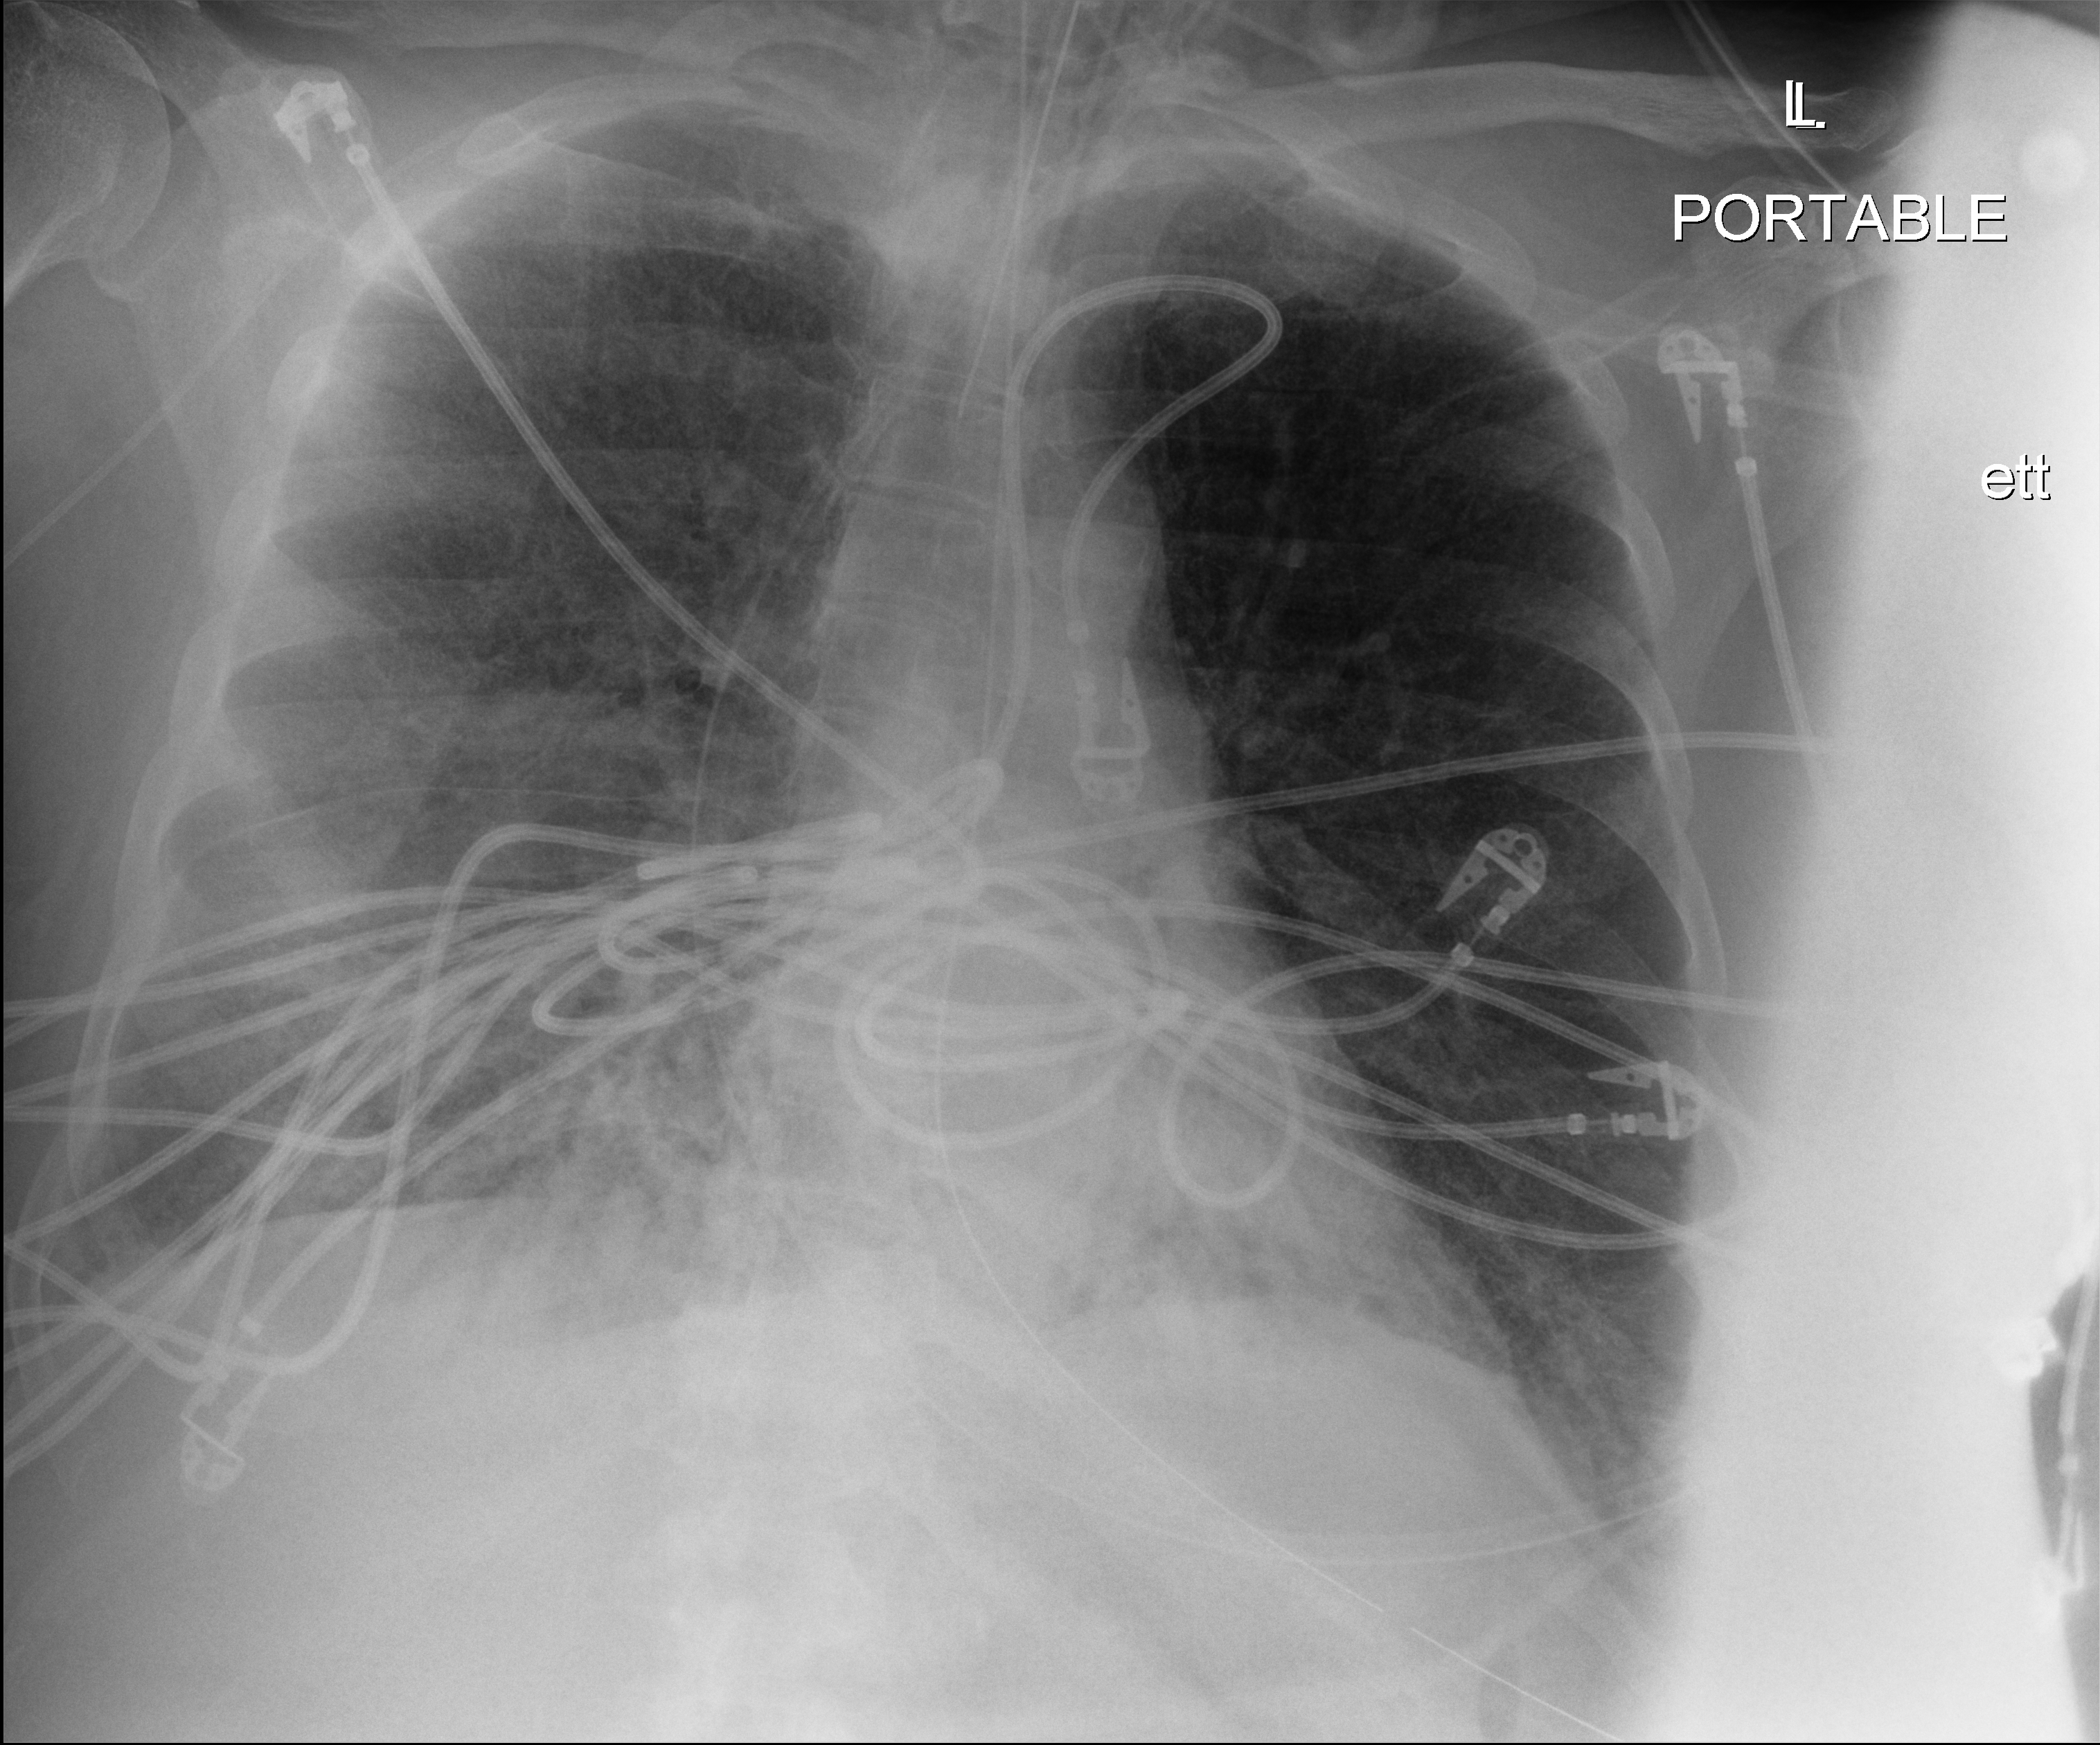
Chest radiograph (digital radiography), anteroposterior (AP) projection. Patient hospitalised with COVID-19; male, aged 60–74 years.
From the hospital-stay record, not from the radiograph (when in the stay this image was taken is not recorded): chronic kidney disease (admission record): no; mechanically ventilated during this hospital stay: yes.